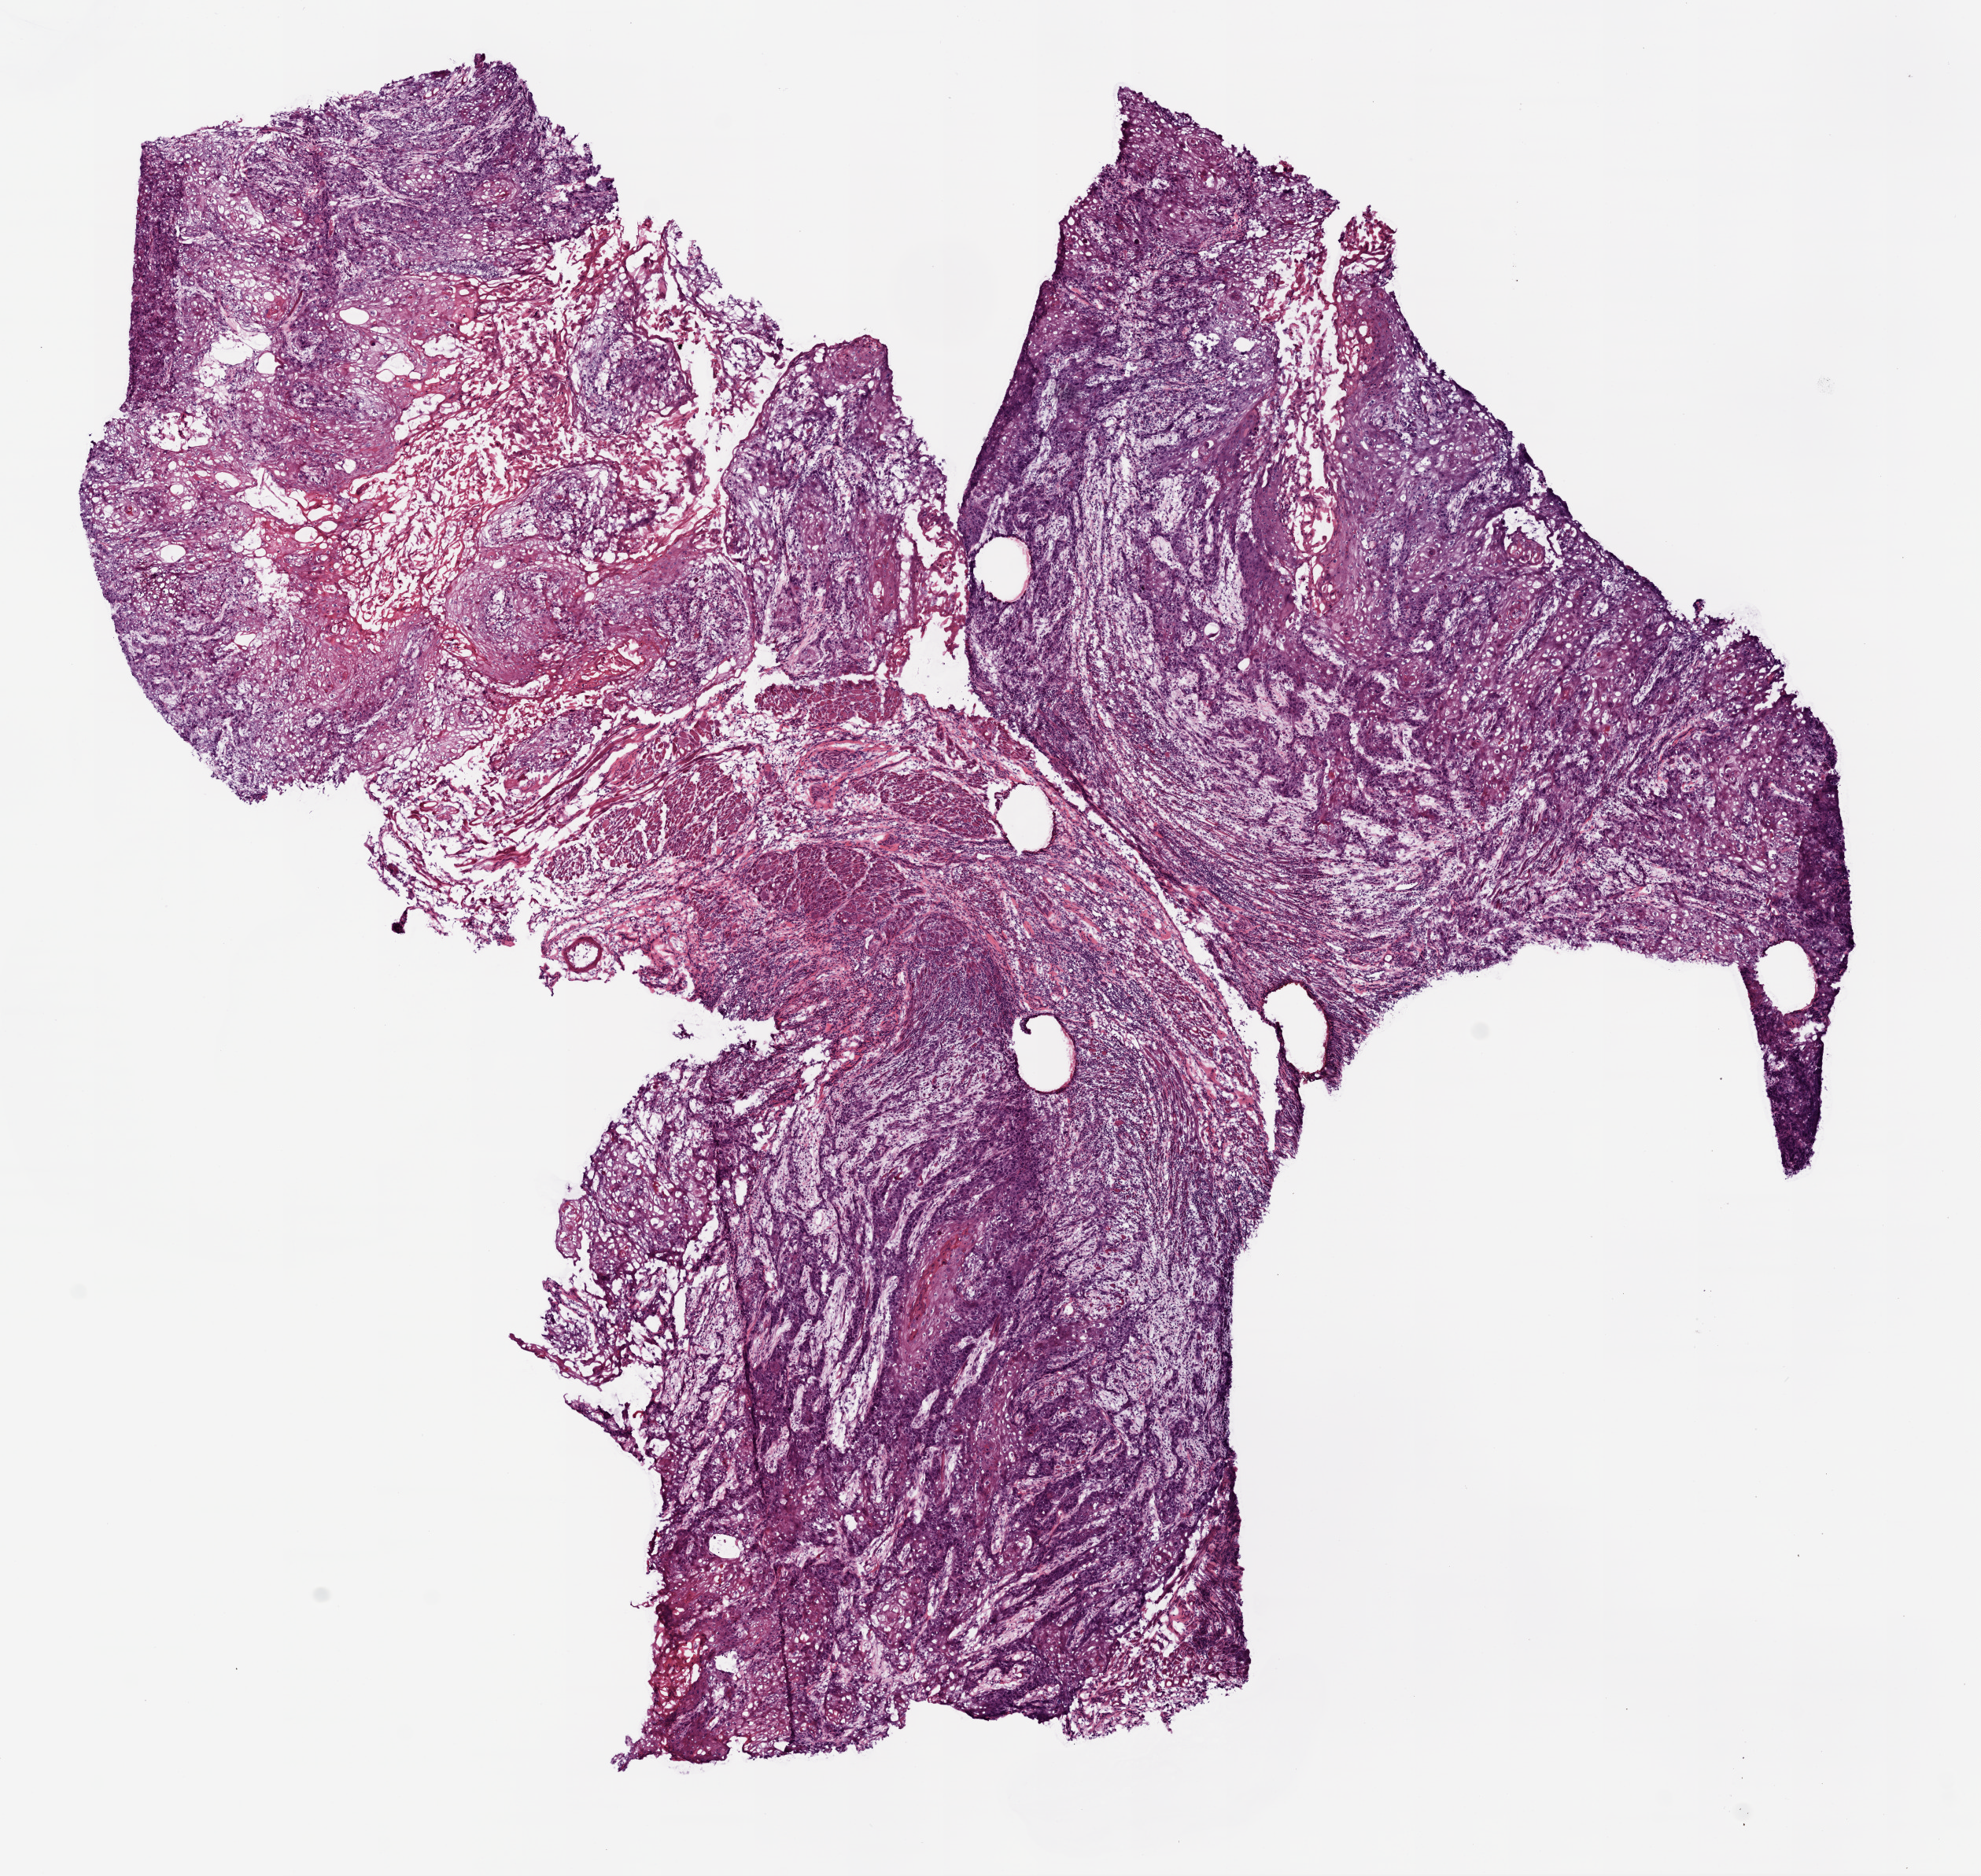
H&E-stained whole-slide image — shown as a low-resolution overview of the whole scanned area (about 10.2 x 9.6 mm), frozen section from the bottom of the tissue portion, primary tumour sample from the head and neck. Male, age 53 years at initial diagnosis. Histologic grade: G2 (moderately differentiated). Composition of this section per pathologist review: tumour nuclei 70%, normal cells 0%, stromal cells 60%, necrosis 0%.
- diagnosis: Squamous cell carcinoma, NOS (tongue, NOS)
- lymph nodes positive (case pathology): 2 of 26 examined
- AJCC pathologic stage: IVA